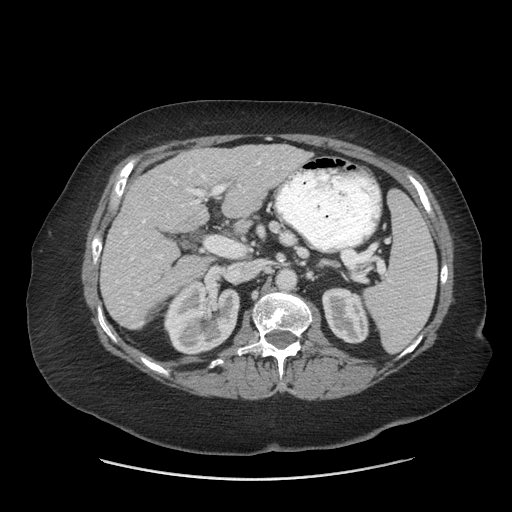
Contrast-enhanced abdominal CT (liver protocol), one axial slice. Position 32 of 69 along the scan axis. Reconstruction kernel STANDARD. Soft-tissue window (W 400 / L 40 HU). 2.5 mm slice thickness. 512 × 512 image matrix. From the clinical record (not read from this slice): diagnosis: hepatocellular carcinoma (patient treated with transarterial chemoembolisation; whether this scan precedes or follows treatment is not stated here); TNM stage (as recorded): Stage-IIIB; Child-Pugh class: A; tumour differentiation: moderately differentiated.
Structures marked on this image (semi-automatic segmentation, software-assisted and operator-edited):
- liver parenchyma outside the tumour (the mass and vessels are separate outlines, so this box may not span the whole liver): box from (x=100, y=144) to (x=311, y=328) px
- liver vessels: (x=116, y=161)–(x=284, y=324)